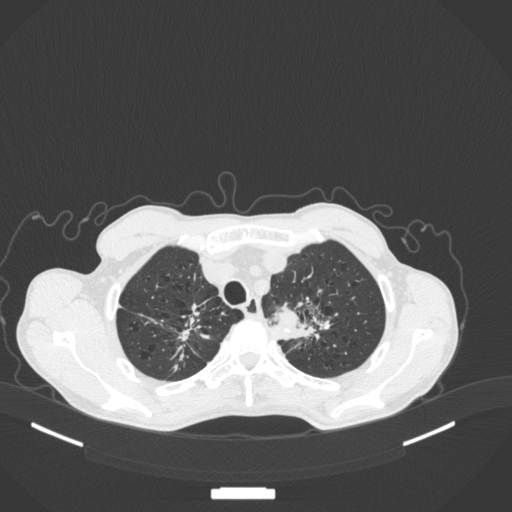
Chest CT, one axial slice; position 361 of 394 along the scan axis; reconstruction kernel B31f; 120 kVp; lung window (W 1500 / L -600 HU); 1 mm slice thickness; 512 × 512 image matrix, field of view 400 × 400 mm. Male patient, age 65 years. From the clinical record (not read from this slice): clinical TNM (as recorded): T2b N0 M0; histopathological grade: G2.
Outlined on this slice (rectangle marked by the reading radiologist):
- lung tumour (recorded histology: adenocarcinoma): bounding box <271,301,304,330> (left, top, right, bottom; pixels)